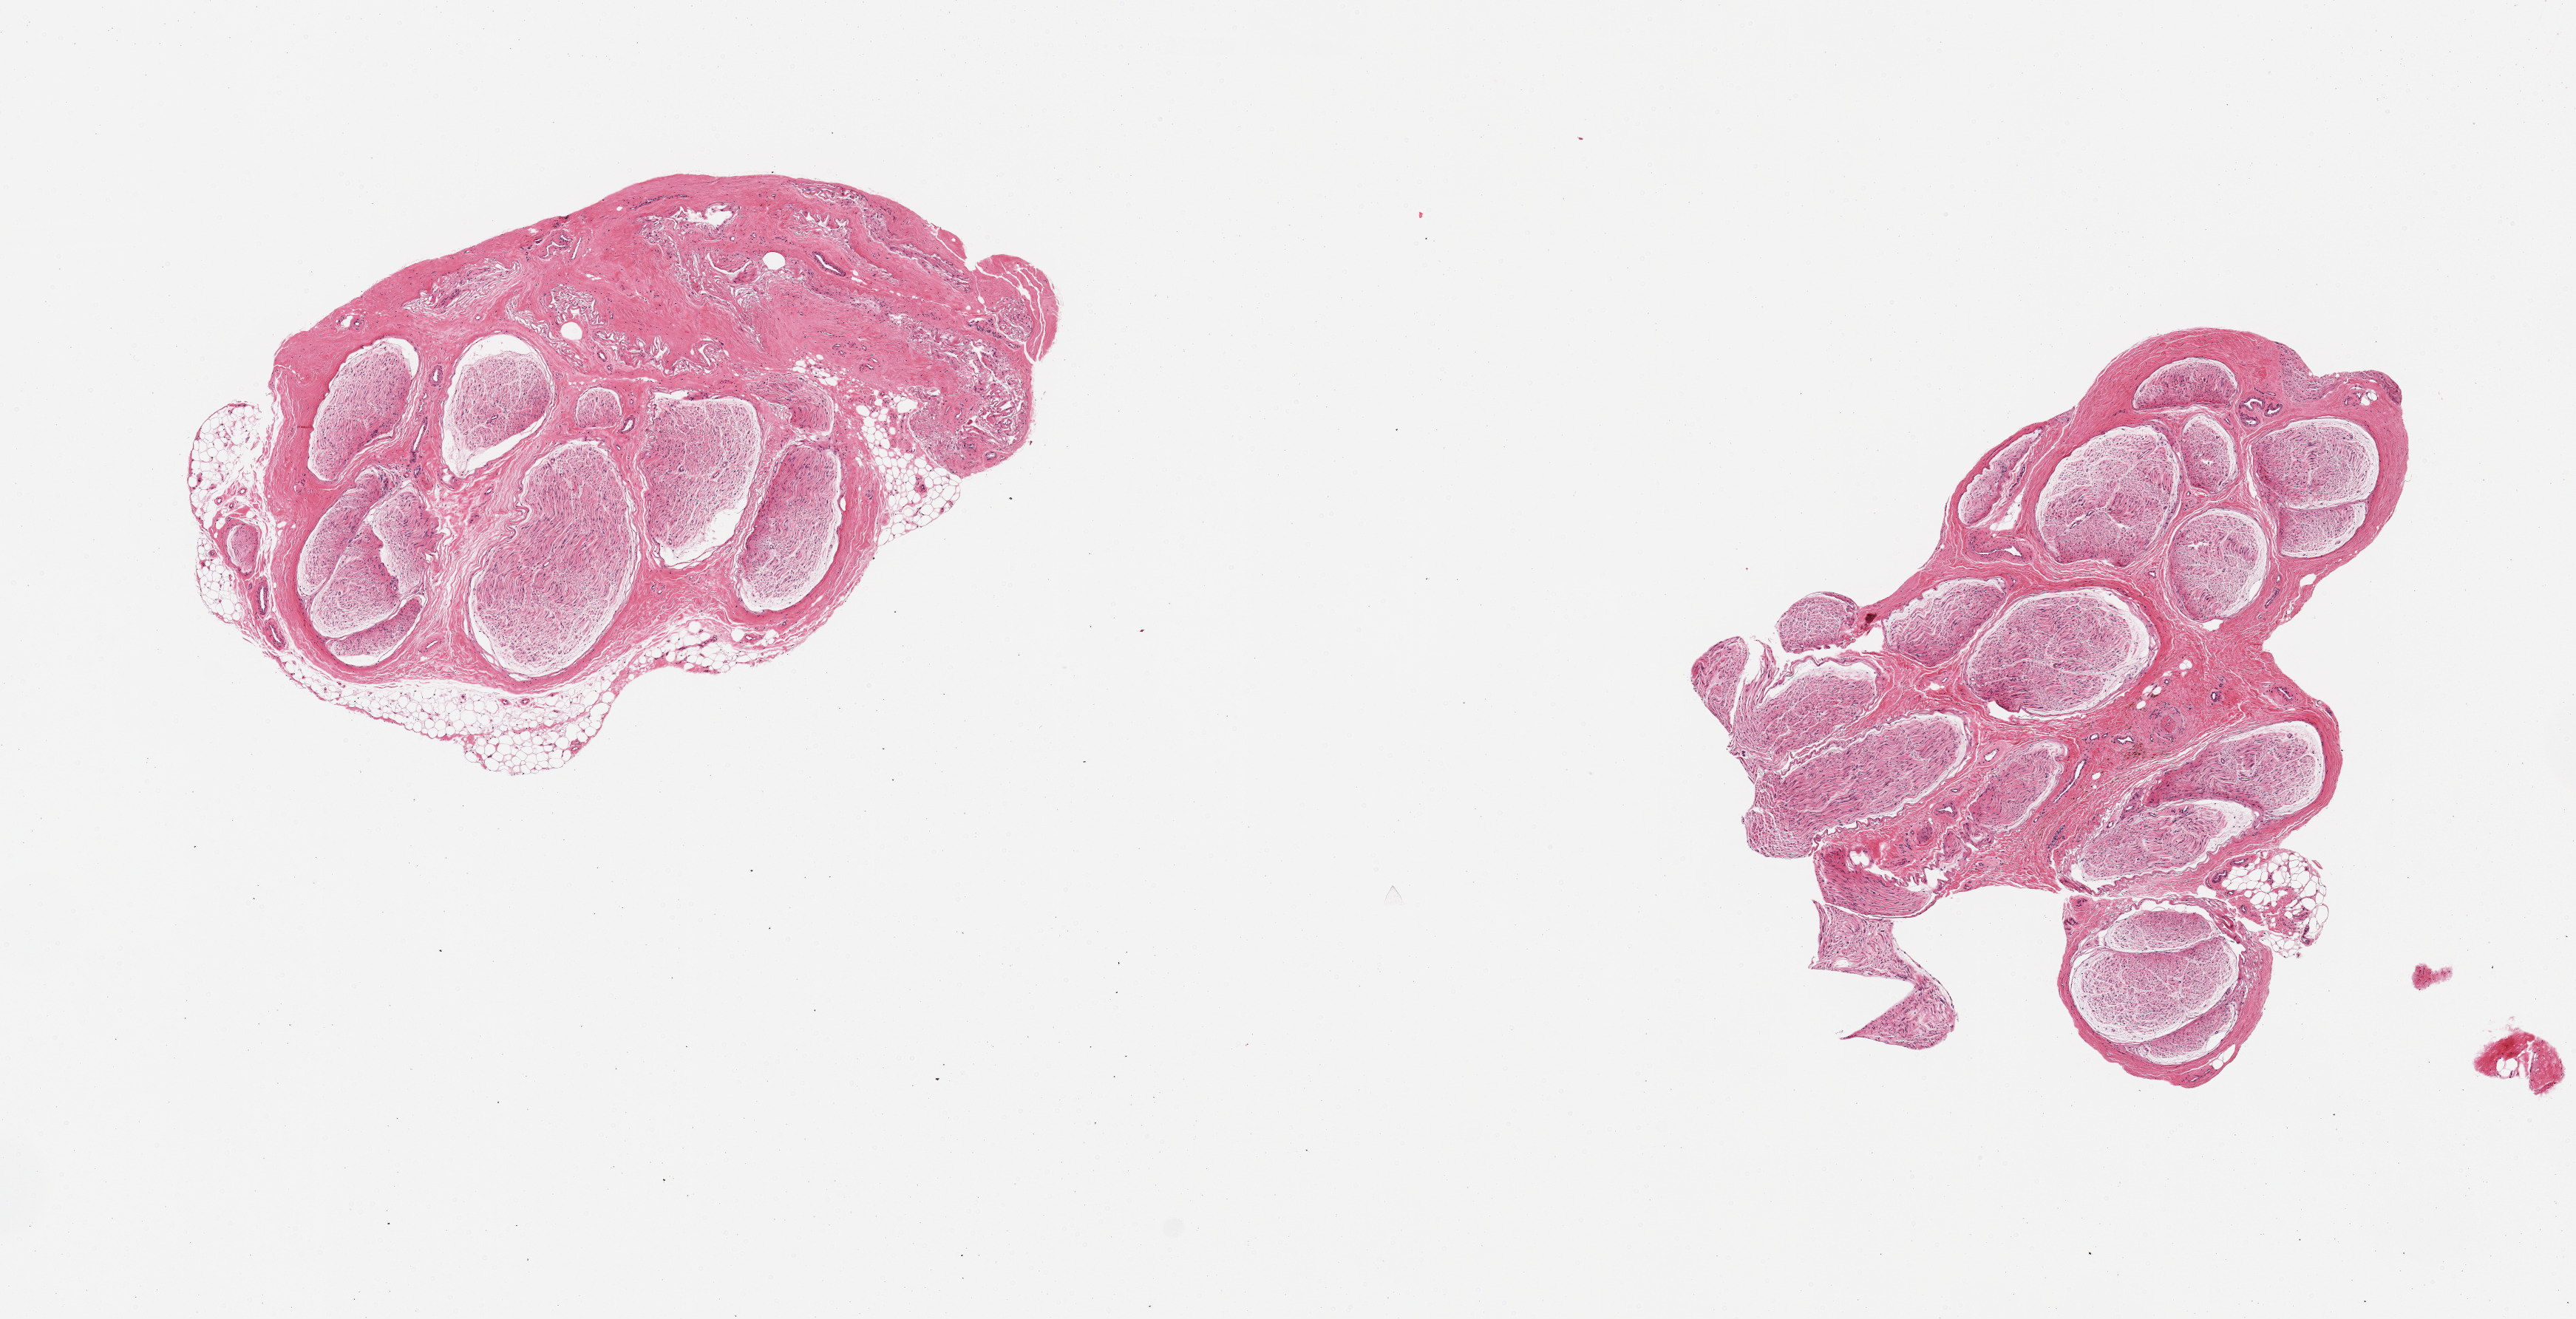
Digitized hematoxylin and eosin (H&E)-stained section — whole scanned area (about 13.8 x 7.1 mm, from a 20x scan) shown as a low-resolution overview. PAXgene-fixed, paraffin-embedded tissue. Sampled site (target tissue): tibial nerve. Donor tissue sample. Donor sex: female.
- pathologist's review note for this sample: 2 pieces, minute nubbins adherent fat on one (~0.3mm), good clean specimens